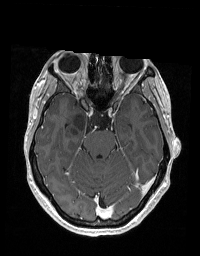
Brain MRI from a brain-tumour surgery series, one axial slice. Position 122 of 192 along the scan axis. T1-weighted post-contrast. 1 mm slice thickness. 200 × 256 image matrix, field of view 195 × 250 mm. Case-level facts recorded for this patient, not image findings: histopathology: Glioblastoma; WHO grade: 2; IDH mutation: no.
Annotated regions visible in this slice (manually delineated by an expert):
- tumour: bounding box (x1, y1, x2, y2) in pixels: (72, 113, 102, 135)